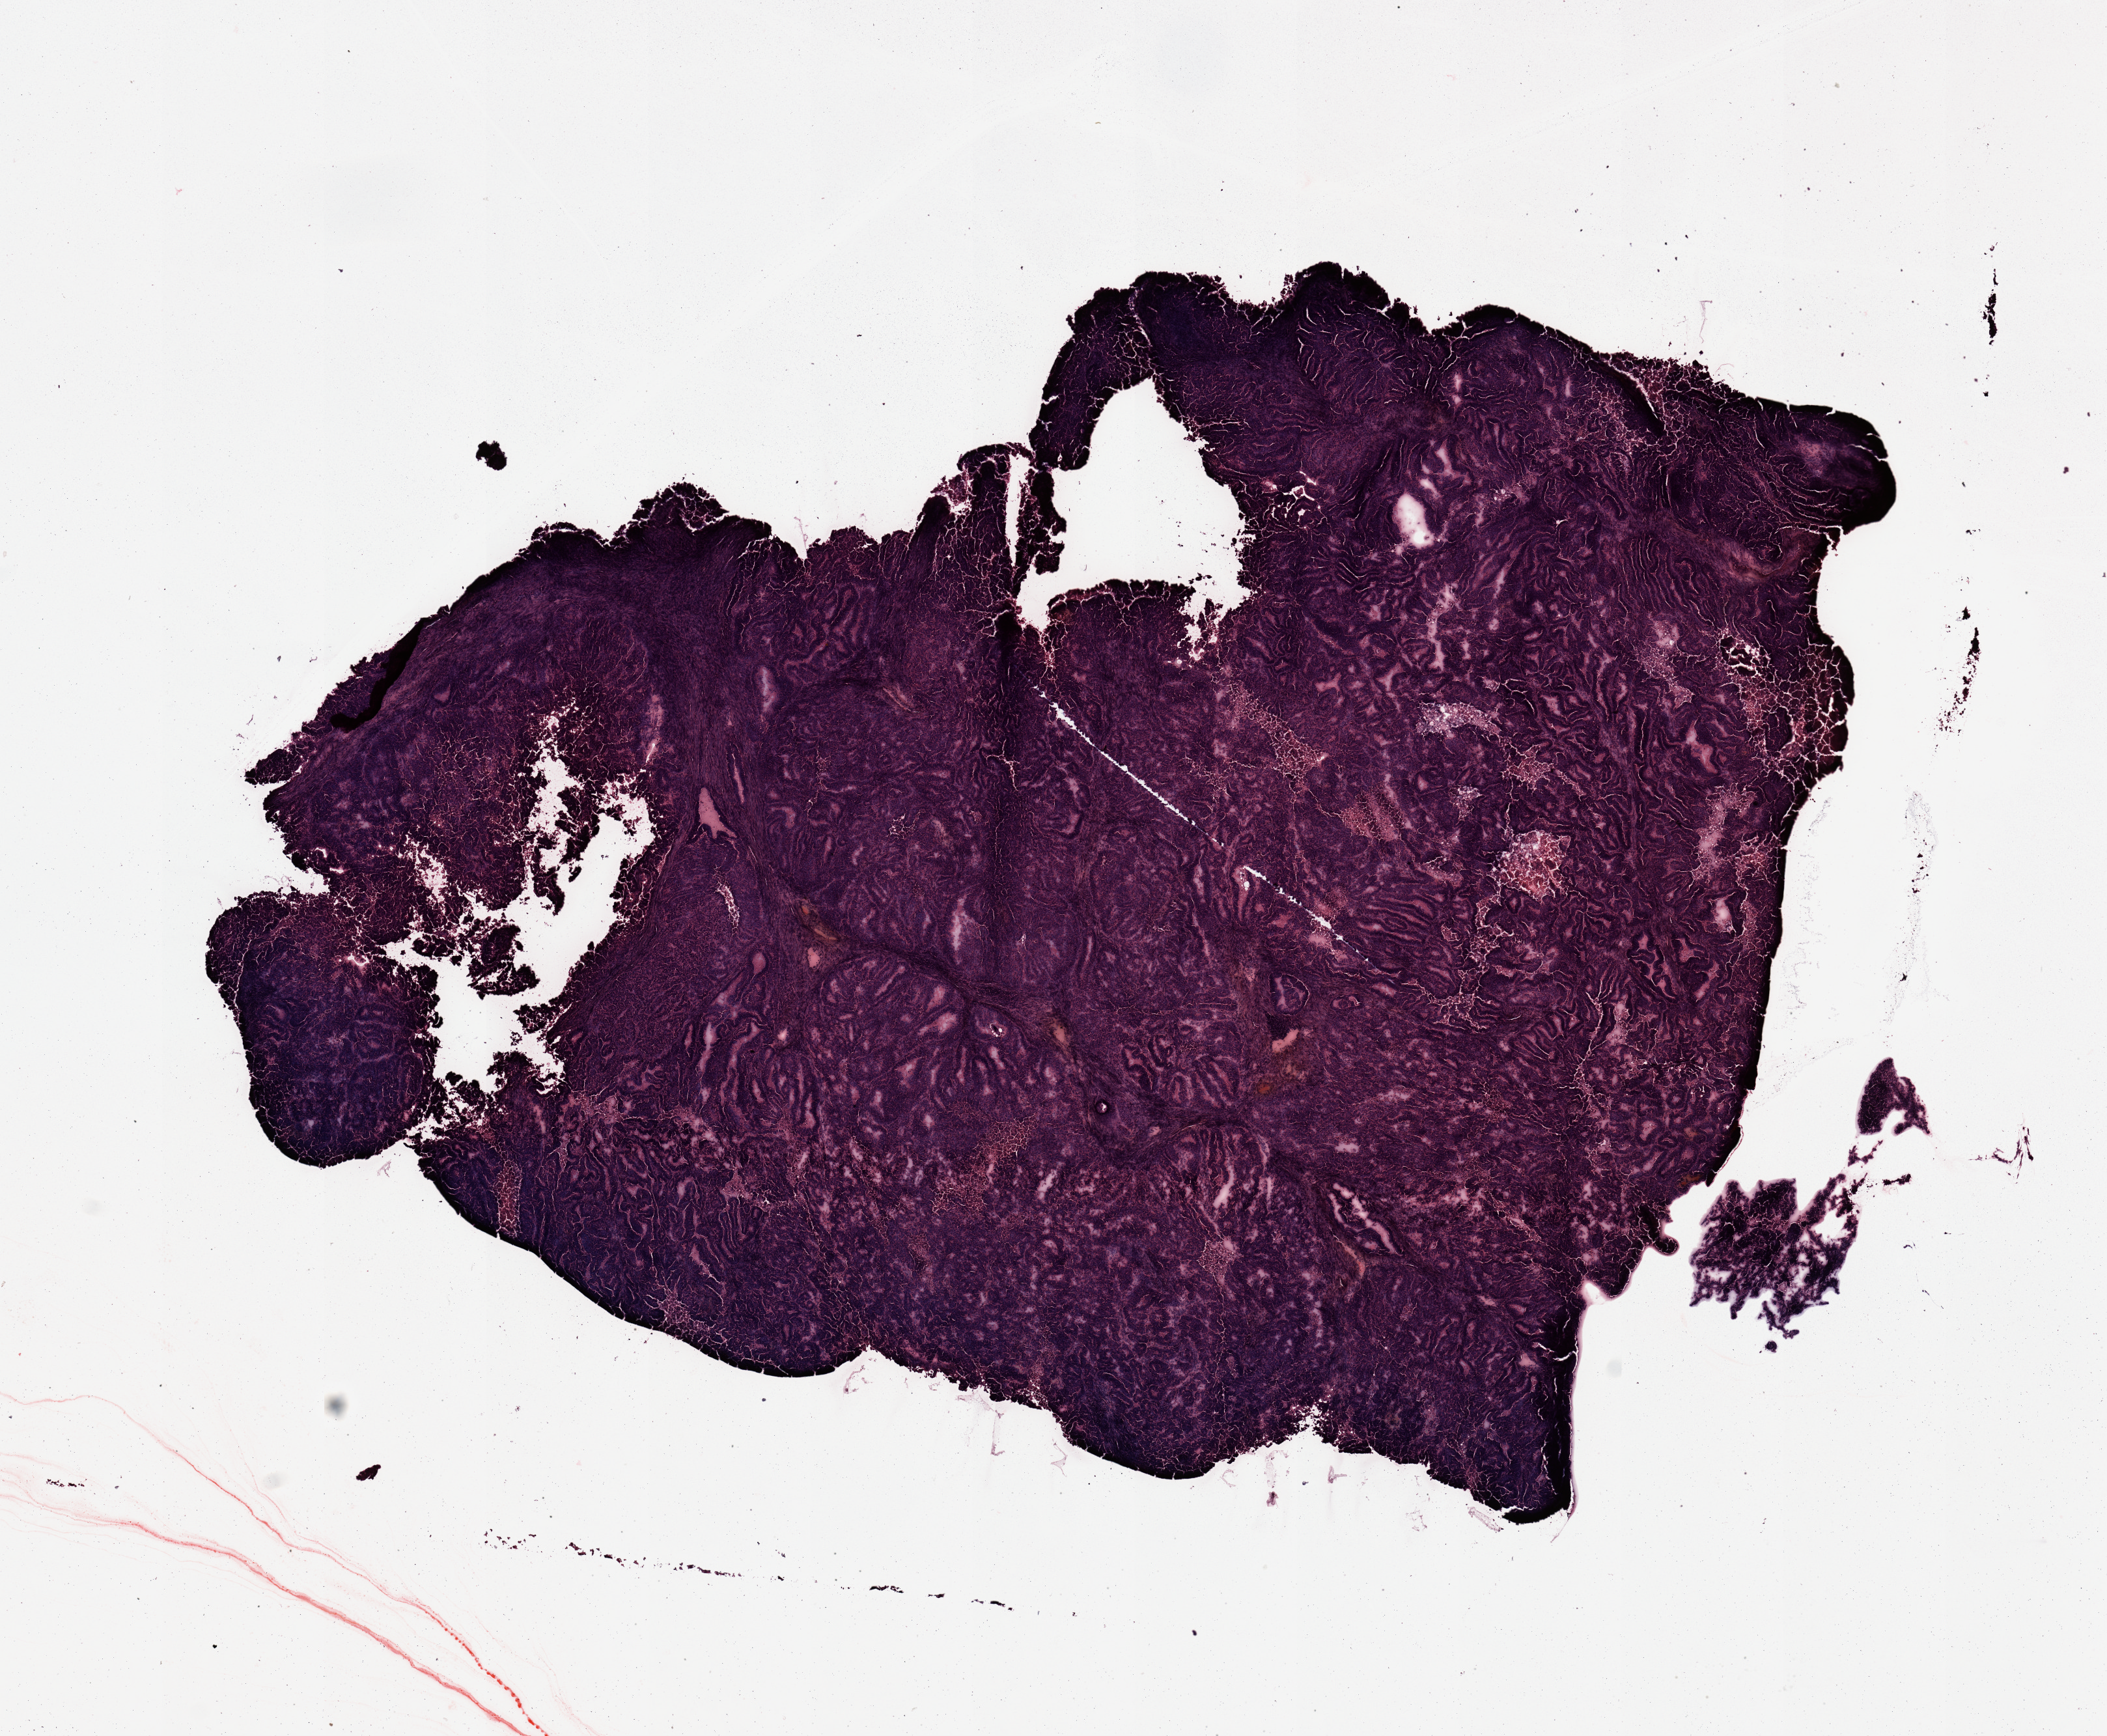
Digitized H&E-stained tissue section (whole slide), a low-resolution overview of the entire scanned area, about 12.8 x 10.5 mm (slide scanned at 20x), uterus, tumour tissue. Female, 78 y/o. Histologic grade: G2 (moderately differentiated).
Diagnosis: Endometrioid adenocarcinoma, NOS. AJCC pathologic stage: I.